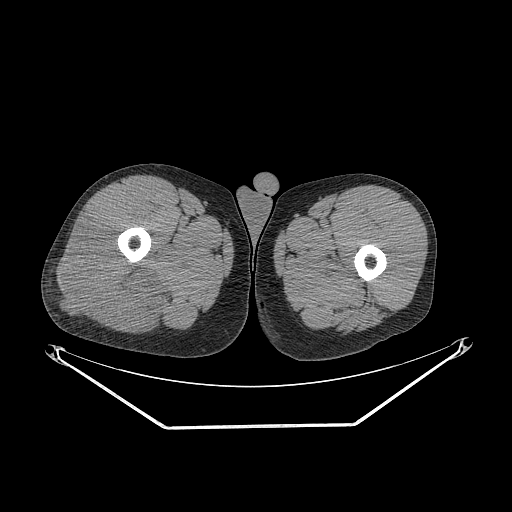
CT of an extremity soft-tissue mass (from a PET/CT study), one axial slice. Slice 258 of 267 in the series (ordered by position). Reconstruction kernel STANDARD. Soft-tissue window (W 400 / L 40 HU). 3.75 mm slice thickness. 512 × 512 image matrix, field of view 500 × 500 mm. Male patient. From the clinical record (not read from this slice): histological type: poorly differentiated synovial sarcoma; grade: high; site of the primary tumour: right buttock.
Structures marked on this image (expert contour drawn on MRI and transferred to this co-registered scan by the dataset authors):
- gross tumour volume including surrounding oedema: box from (x=53, y=217) to (x=161, y=332) px
- gross tumour volume (mass): (x=53, y=217)–(x=161, y=332)